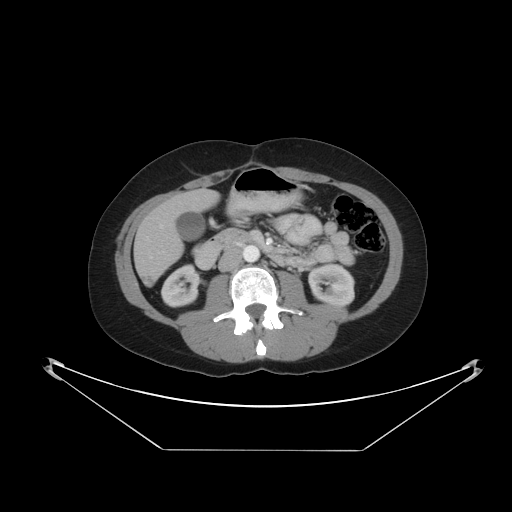
Contrast-enhanced abdominal CT, one axial slice. Slice 15 of 48 in the series (ordered by position). Reconstruction kernel STANDARD. Intravenous contrast given. Soft-tissue window (W 400 / L 40 HU). 5 mm slice thickness. 512 × 512 image matrix. Female patient, age 38 years. Case-level facts recorded for this patient, not image findings: diagnosis: colorectal cancer liver metastases, imaged before liver resection; multiple liver metastases: yes; largest metastasis: 2.5 cm.
Annotated regions visible in this slice (outlined manually by an expert reader):
- liver: box from (x=135, y=191) to (x=218, y=286) px
- planned liver remnant (the part of the liver to remain after resection): (x=171, y=191)–(x=218, y=213)
- liver metastasis: (x=145, y=277)–(x=156, y=285)